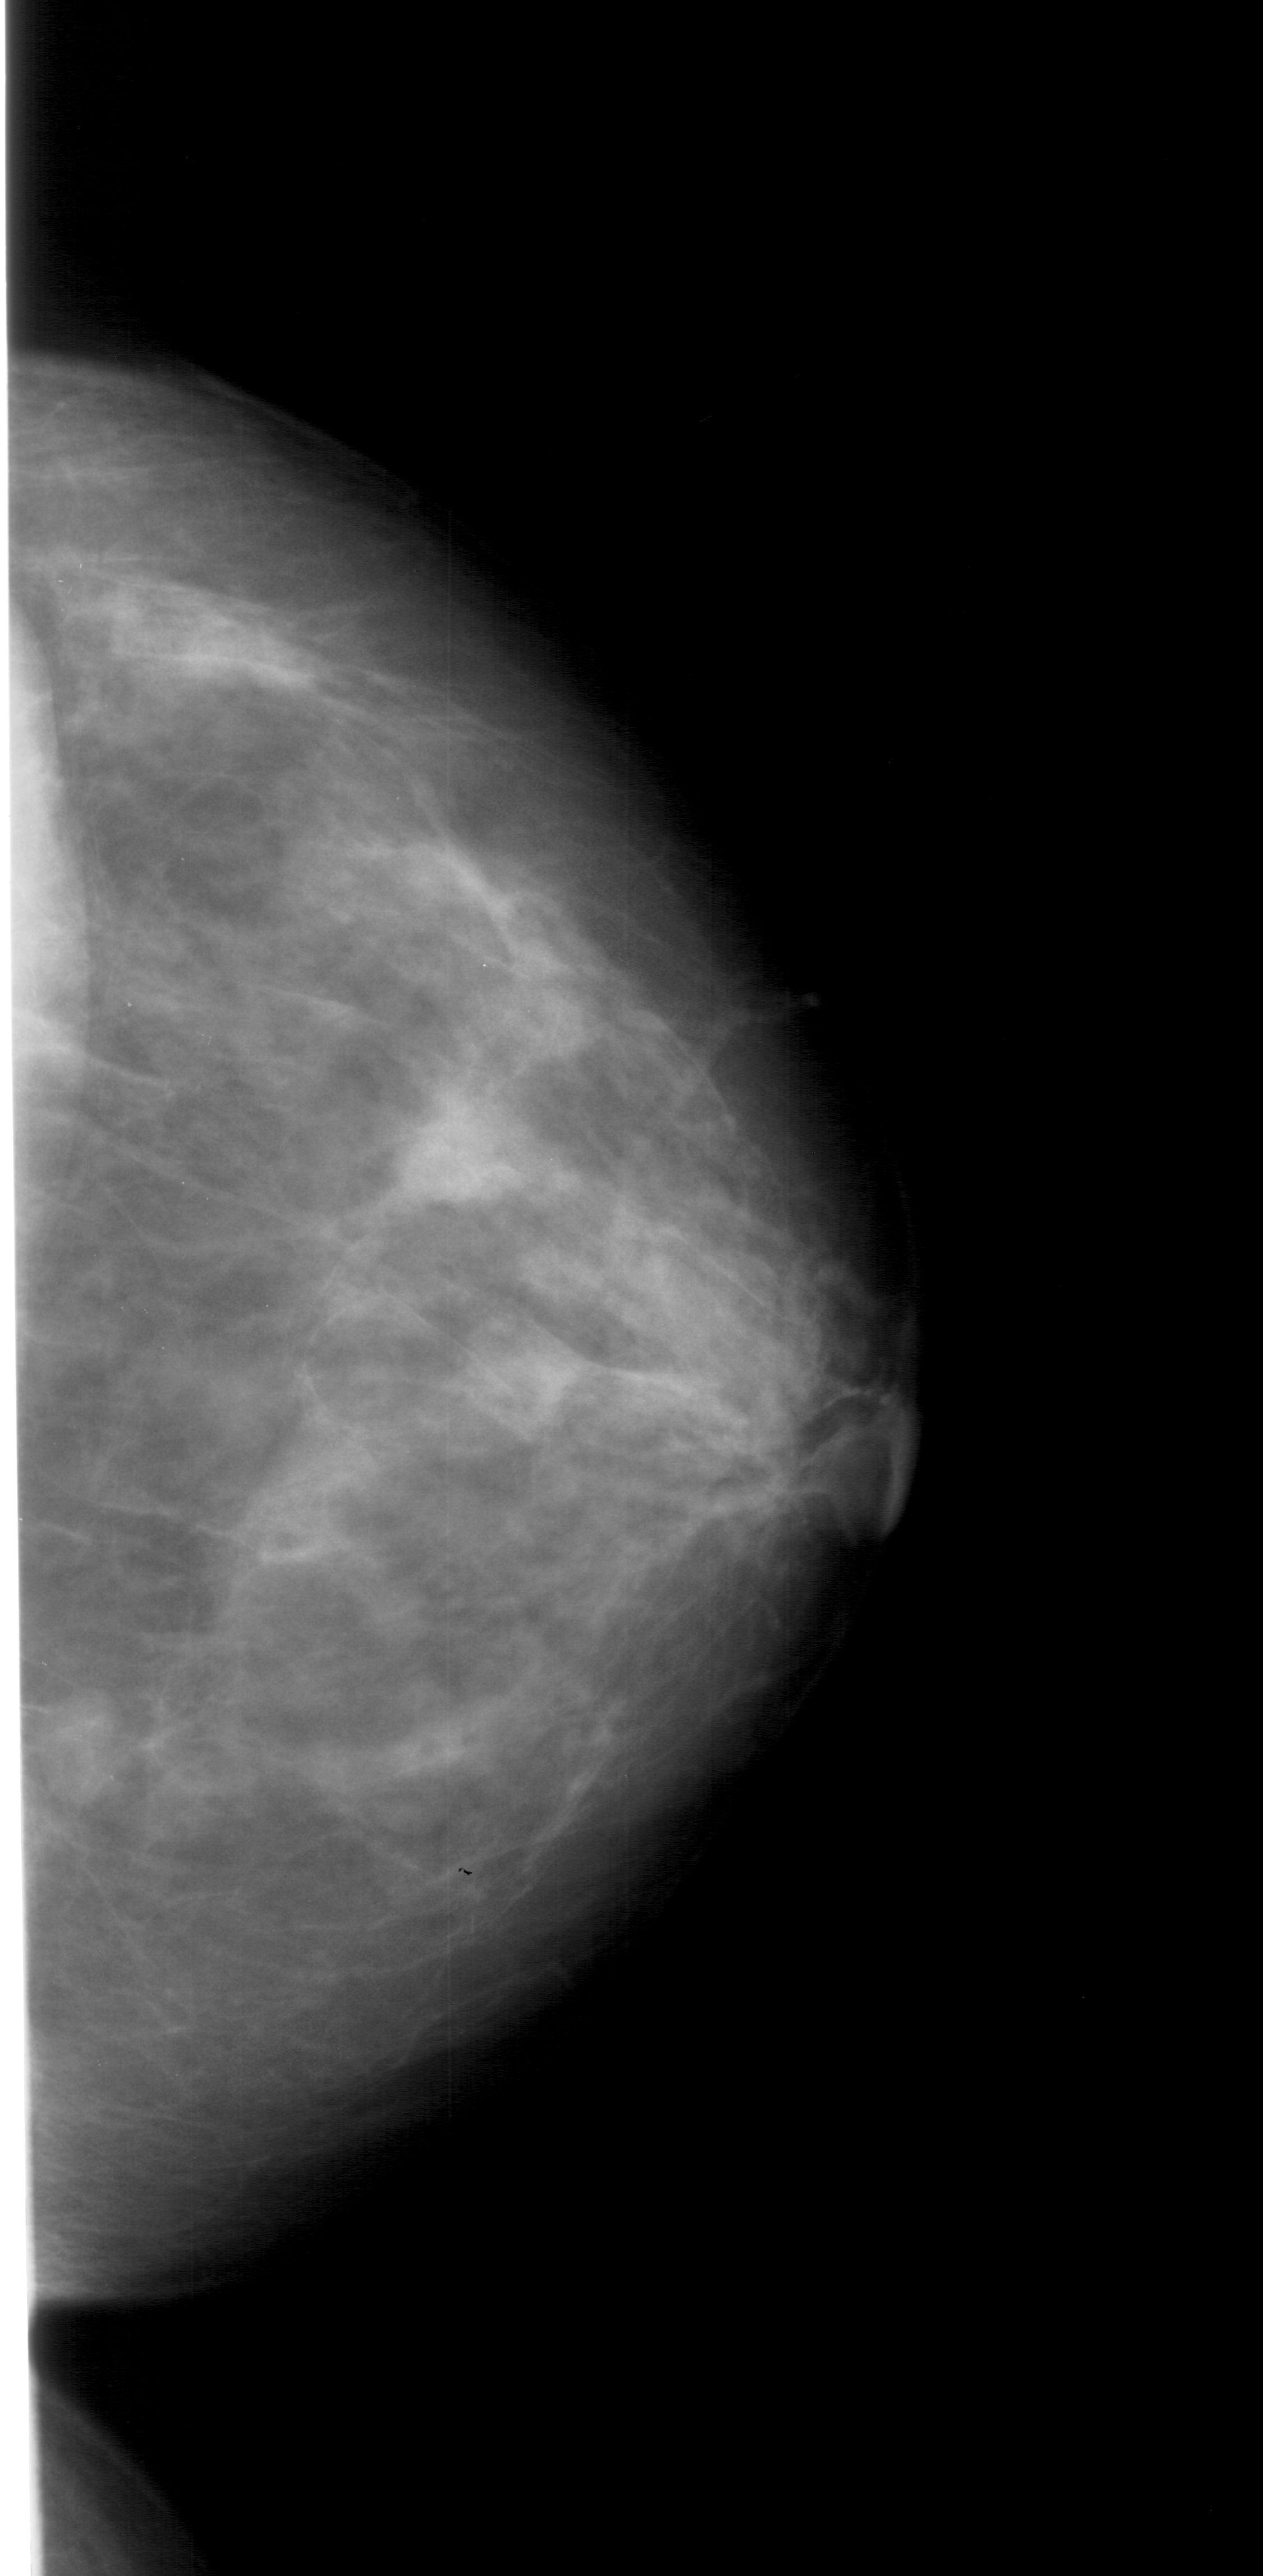
Mammogram (digitized film); right breast; craniocaudal (CC) view; BI-RADS breast density category 3 (scale 1–4).
- Abnormality record for this image: mass, shape lobulated, margins obscured; BI-RADS assessment category 3; subtlety rating 3 on a 1 (subtle) to 5 (obvious) scale; pathology result (as recorded, not read from the image): benign.